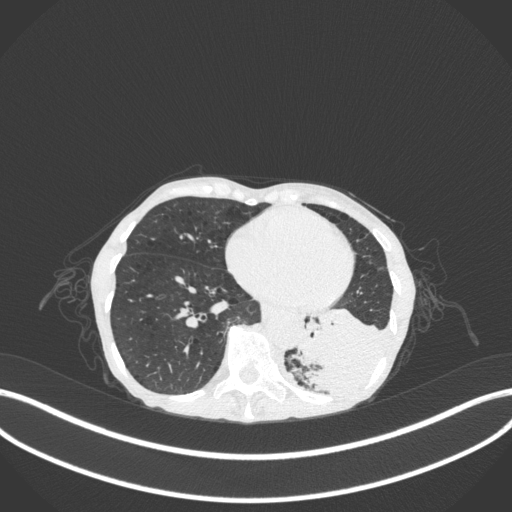
Chest CT, one axial slice; reconstruction kernel B31f; 120 kVp; lung window (W 1500 / L -600 HU); 512 × 512 image matrix, field of view 400 × 400 mm. Patient: female, 70 years. Case-level facts recorded for this patient, not image findings: clinical TNM (as recorded): T3 N0 M0.
Outlined on this slice (rectangle marked by the reading radiologist):
- lung tumour (recorded histology: small cell carcinoma): box from (x=292, y=299) to (x=391, y=406) px